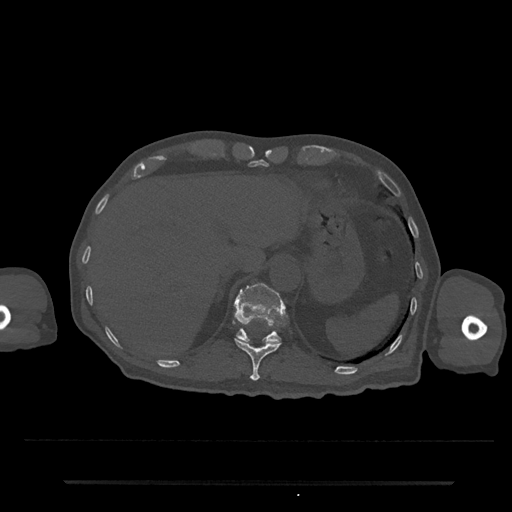
CT including the spine, one axial slice; position 232 of 797 along the scan axis; reconstruction kernel Br40s/3; 120 kVp; bone window (W 1800 / L 400 HU); 0.5 mm slice thickness; 512 × 512 image matrix, field of view 427 × 427 mm. Patient: male, 74 years. From the clinical record (not read from this slice): primary cancer: prostate.
Outlined on this slice (semi-automatic segmentation, software-assisted and operator-edited):
- T11 vertebra: bounding box [x1, y1, x2, y2] px = [235, 338, 282, 381]
- T12 vertebra: [234, 283, 283, 344]